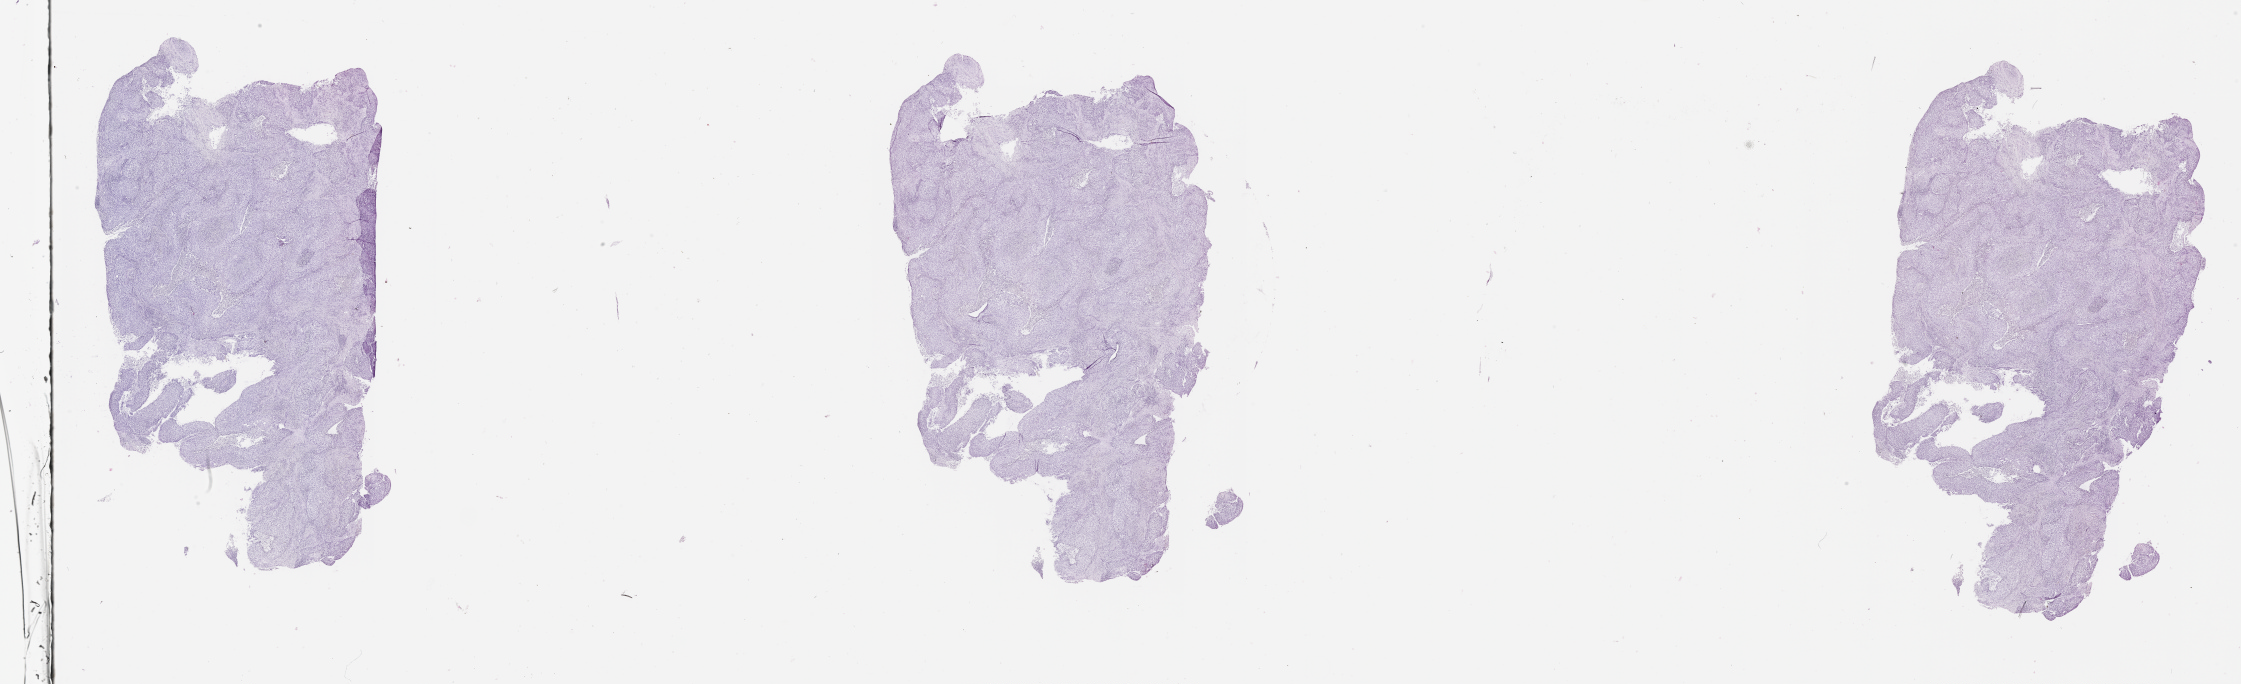
Digitized H&E tissue section (whole slide) — whole scanned area (about 36.1 x 11.0 mm, slide scanned at 20x) shown as a low-resolution overview, tumour tissue sample, lung. 66-year-old male patient.
Patient diagnosis (cohort enrolment): squamous cell carcinoma (lung).